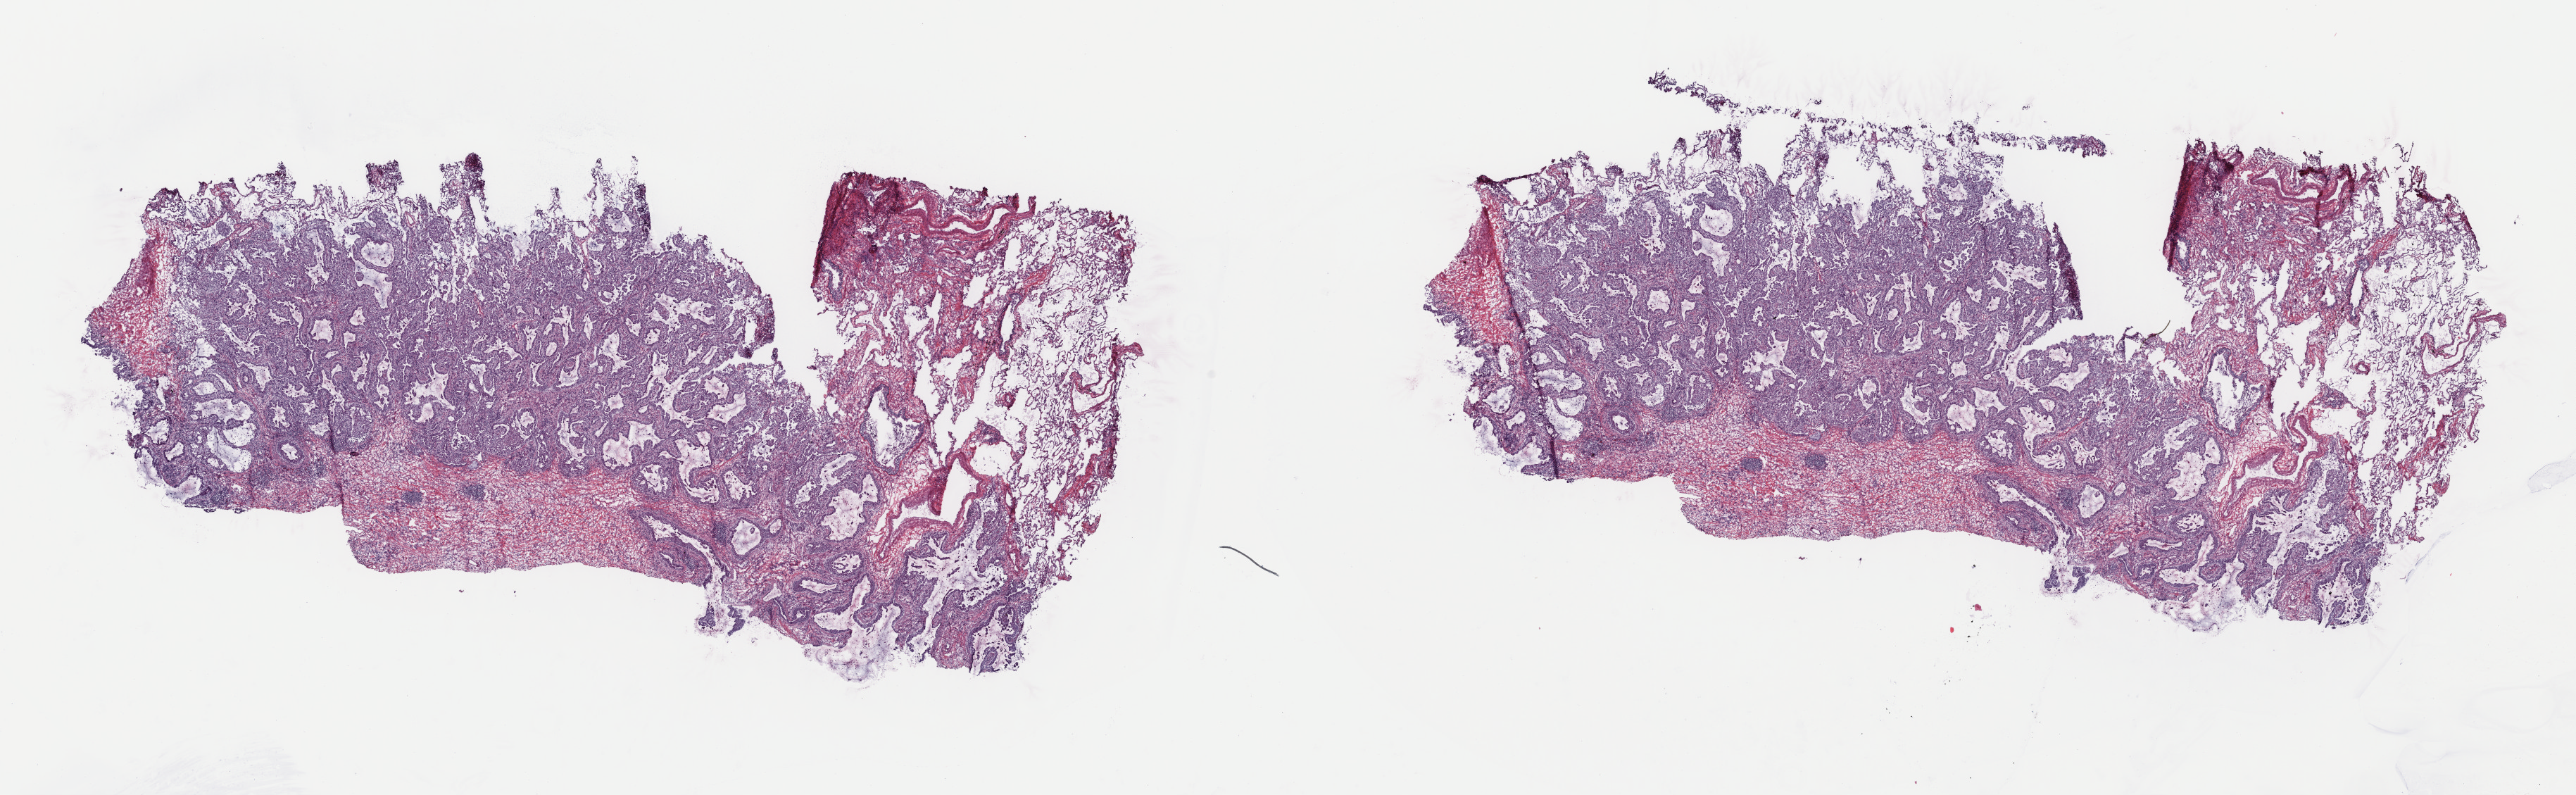
Hematoxylin and eosin (H&E) stained whole-slide image — whole scanned area (about 28.9 x 8.9 mm, slide scanned at 40x) shown as a low-resolution overview; frozen section from the top of the tissue portion; primary tumour sample from the lung. Male, age 83 years at initial diagnosis. Pathologist review of this section (percent, as recorded): tumour cells 35%, tumour nuclei 75%, normal cells 18%, stromal cells 27%, necrosis 20%. Infiltration values recorded for this section: lymphocyte infiltration 3%, monocyte infiltration 3%, neutrophil infiltration 1%.
Histologic diagnosis: Adenocarcinoma with mixed subtypes (upper lobe, lung). TNM: T1b N0 M0. AJCC pathologic stage: IA (7th edition).